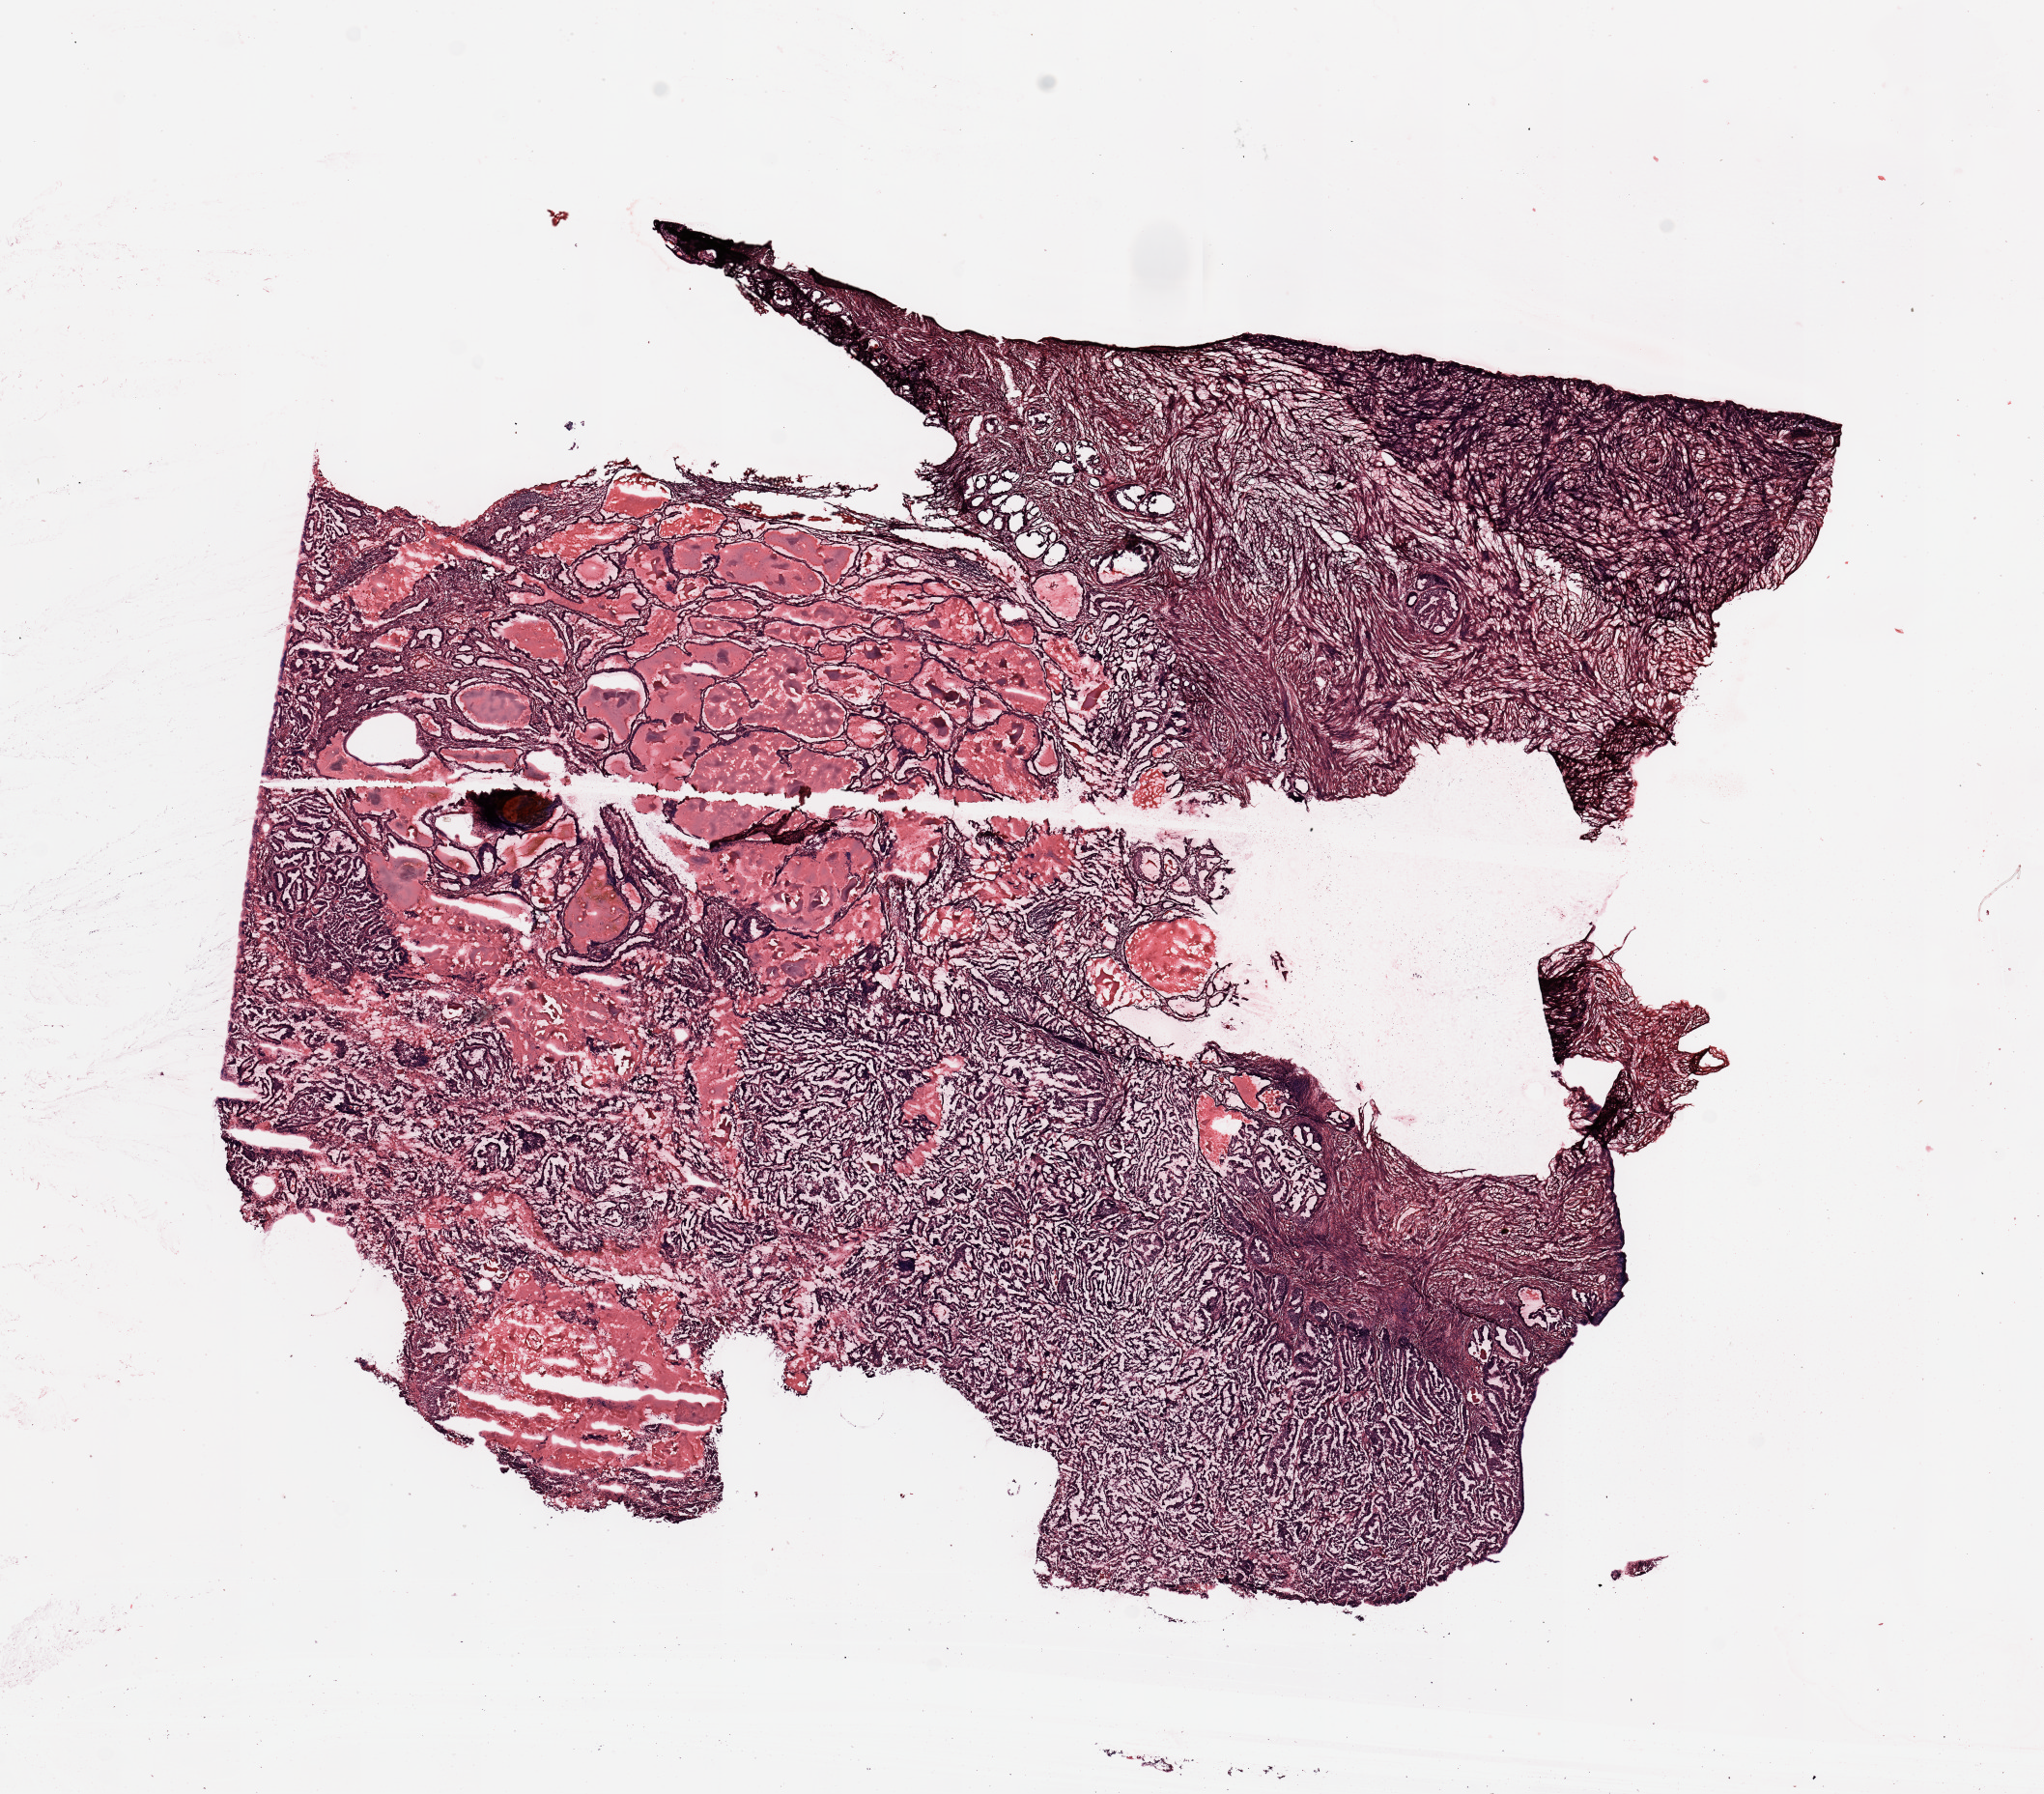
Whole-slide histology image, H&E — whole scanned area (about 16.7 x 14.7 mm) shown as a low-resolution overview. Tumour tissue sample, uterus. Female, 70 y/o. Histologic grade: G2 (moderately differentiated).
- histologic diagnosis: Endometrioid adenocarcinoma, NOS
- AJCC pathologic stage: I